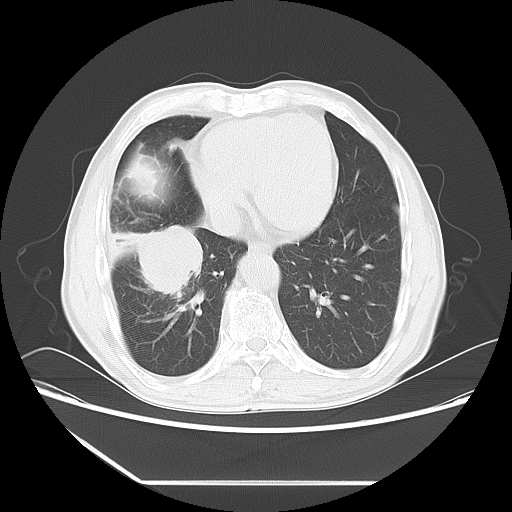
Chest CT, one axial slice; position 21 of 60 along the scan axis; lung window (W 1500 / L -600 HU); 5 mm slice thickness; 512 × 512 image matrix, field of view 386 × 386 mm. Patient: male, 72 years. Case-level facts recorded for this patient, not image findings: clinical TNM (as recorded): T1c N0 M0.
Structures marked on this image (bounding box drawn by a radiologist):
- lung tumour (recorded histology: squamous cell carcinoma): bounding box [x1, y1, x2, y2] px = [103, 218, 209, 317]